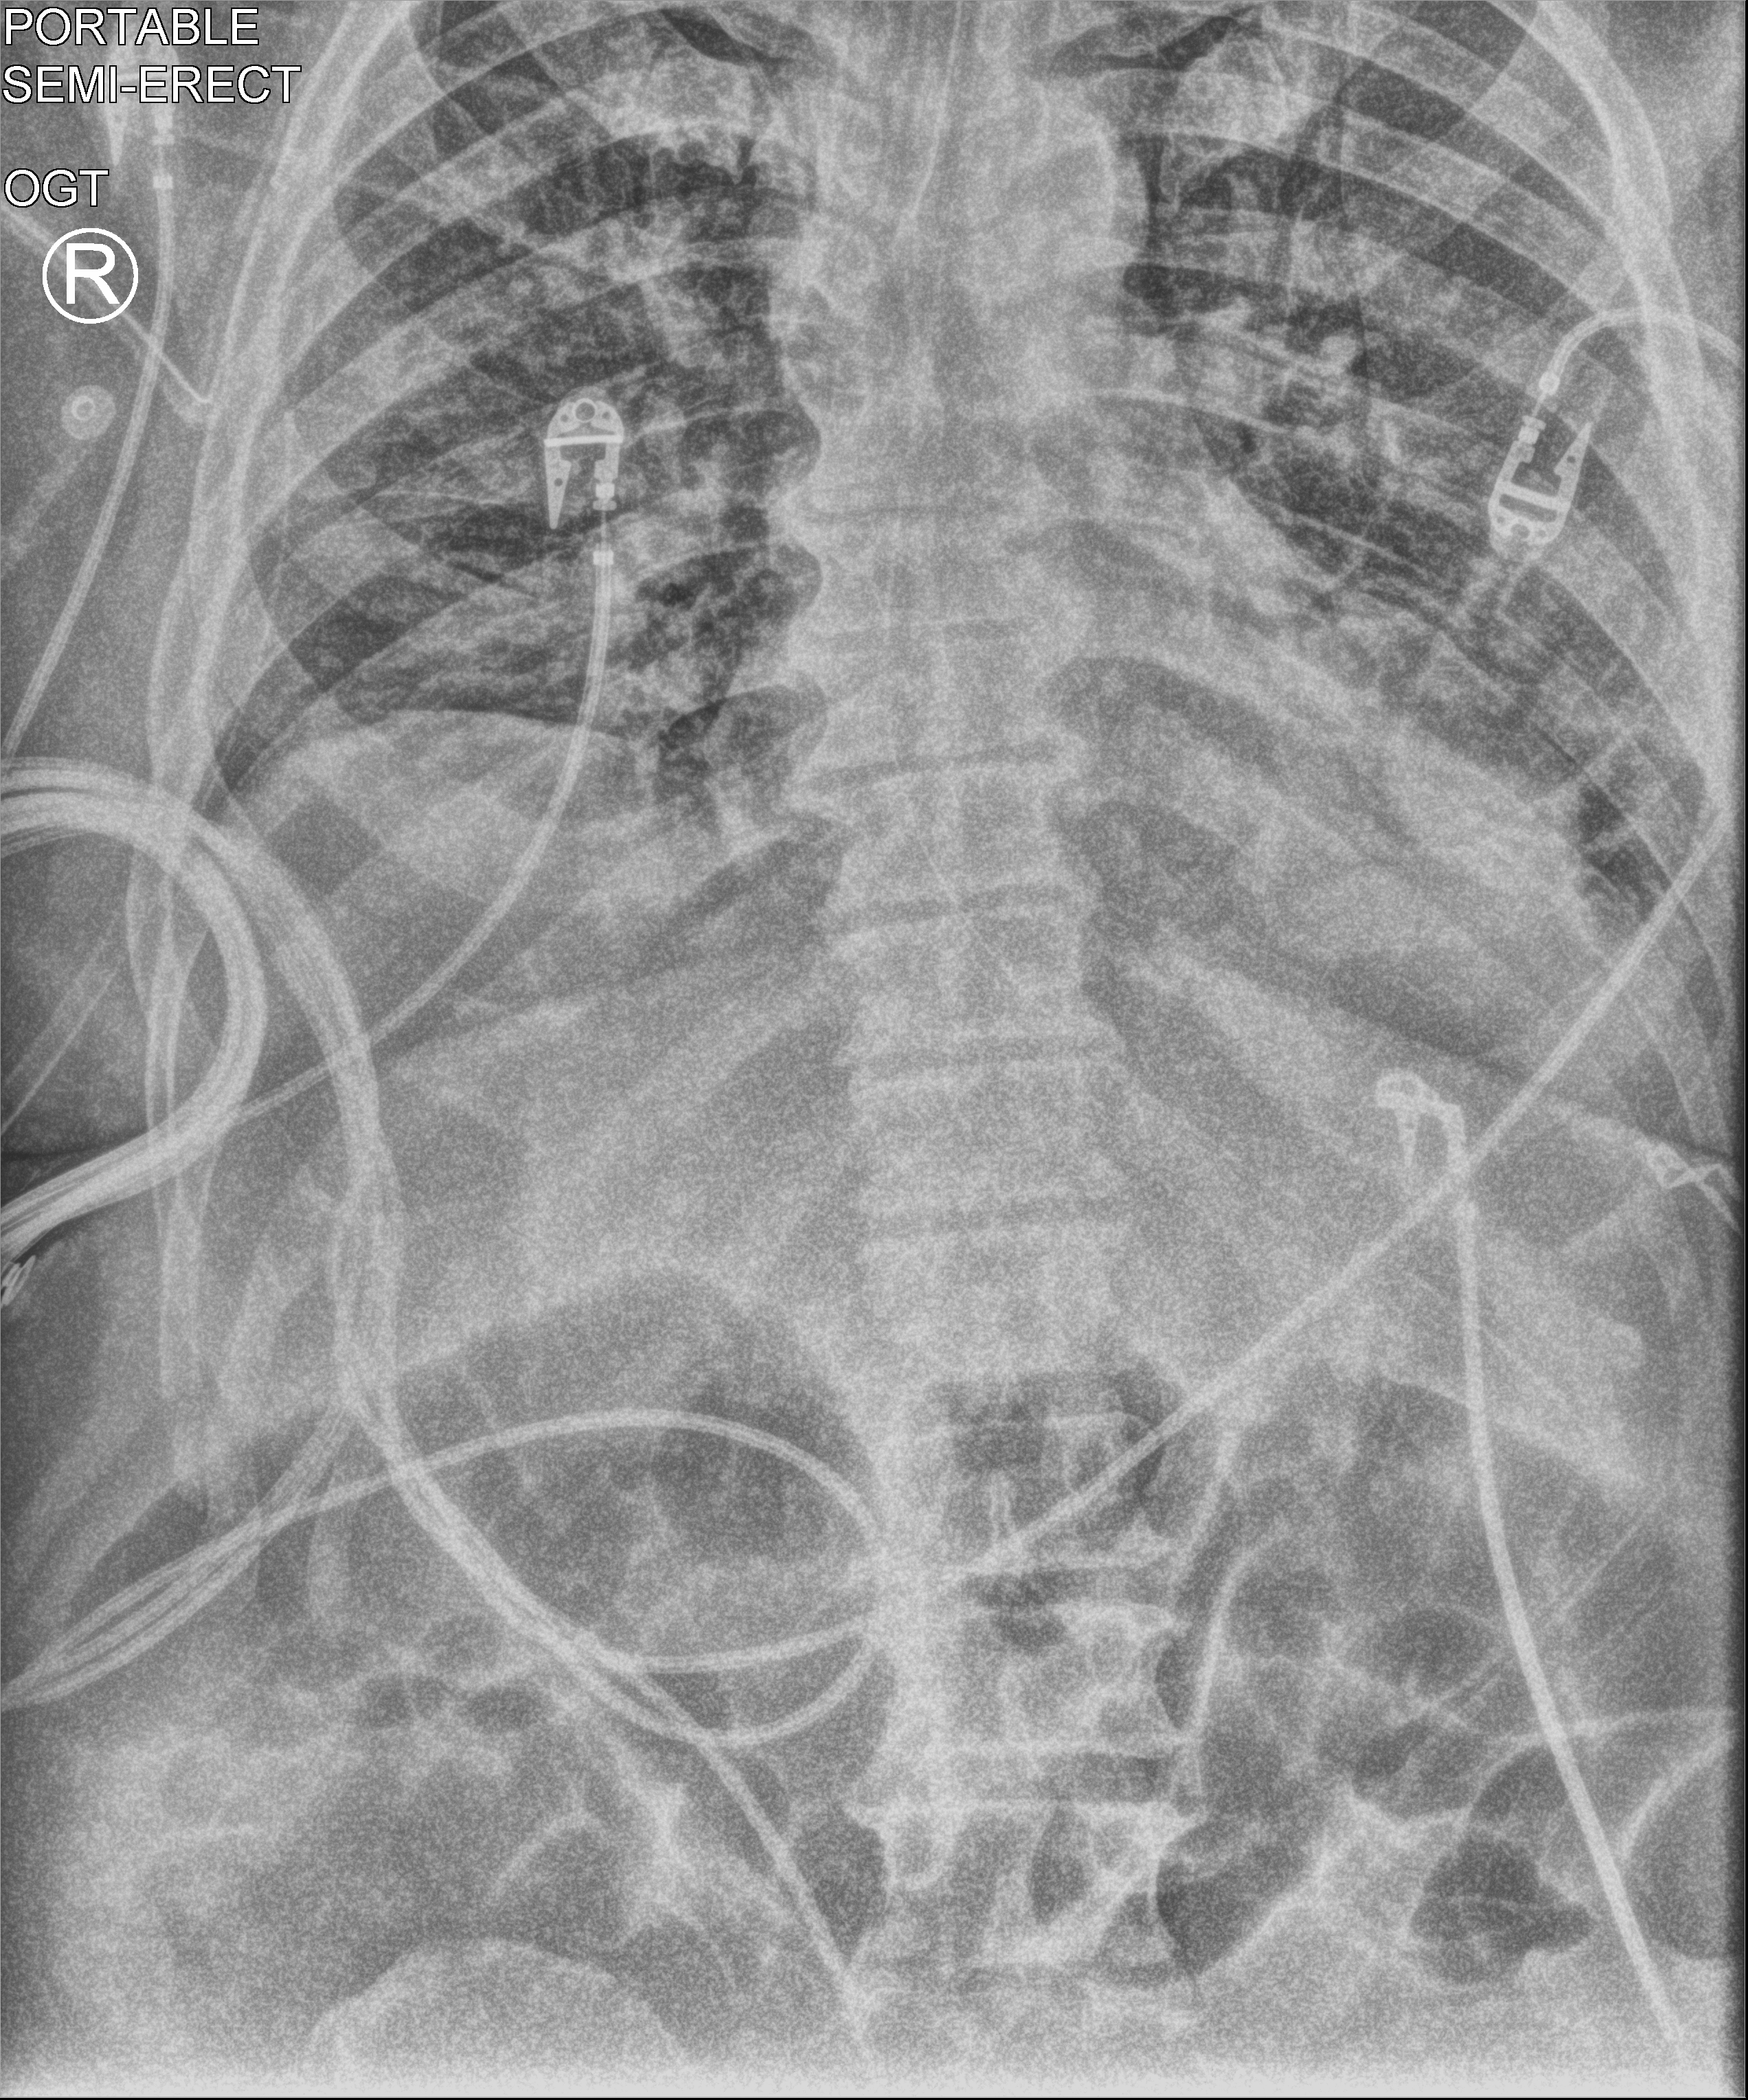
Chest X-ray (portable), anteroposterior (AP) projection. Patient hospitalised with COVID-19; male, aged 18–59 years.
From the hospital-stay record, not from the radiograph (when in the stay this image was taken is not recorded): mechanically ventilated during this hospital stay: yes.